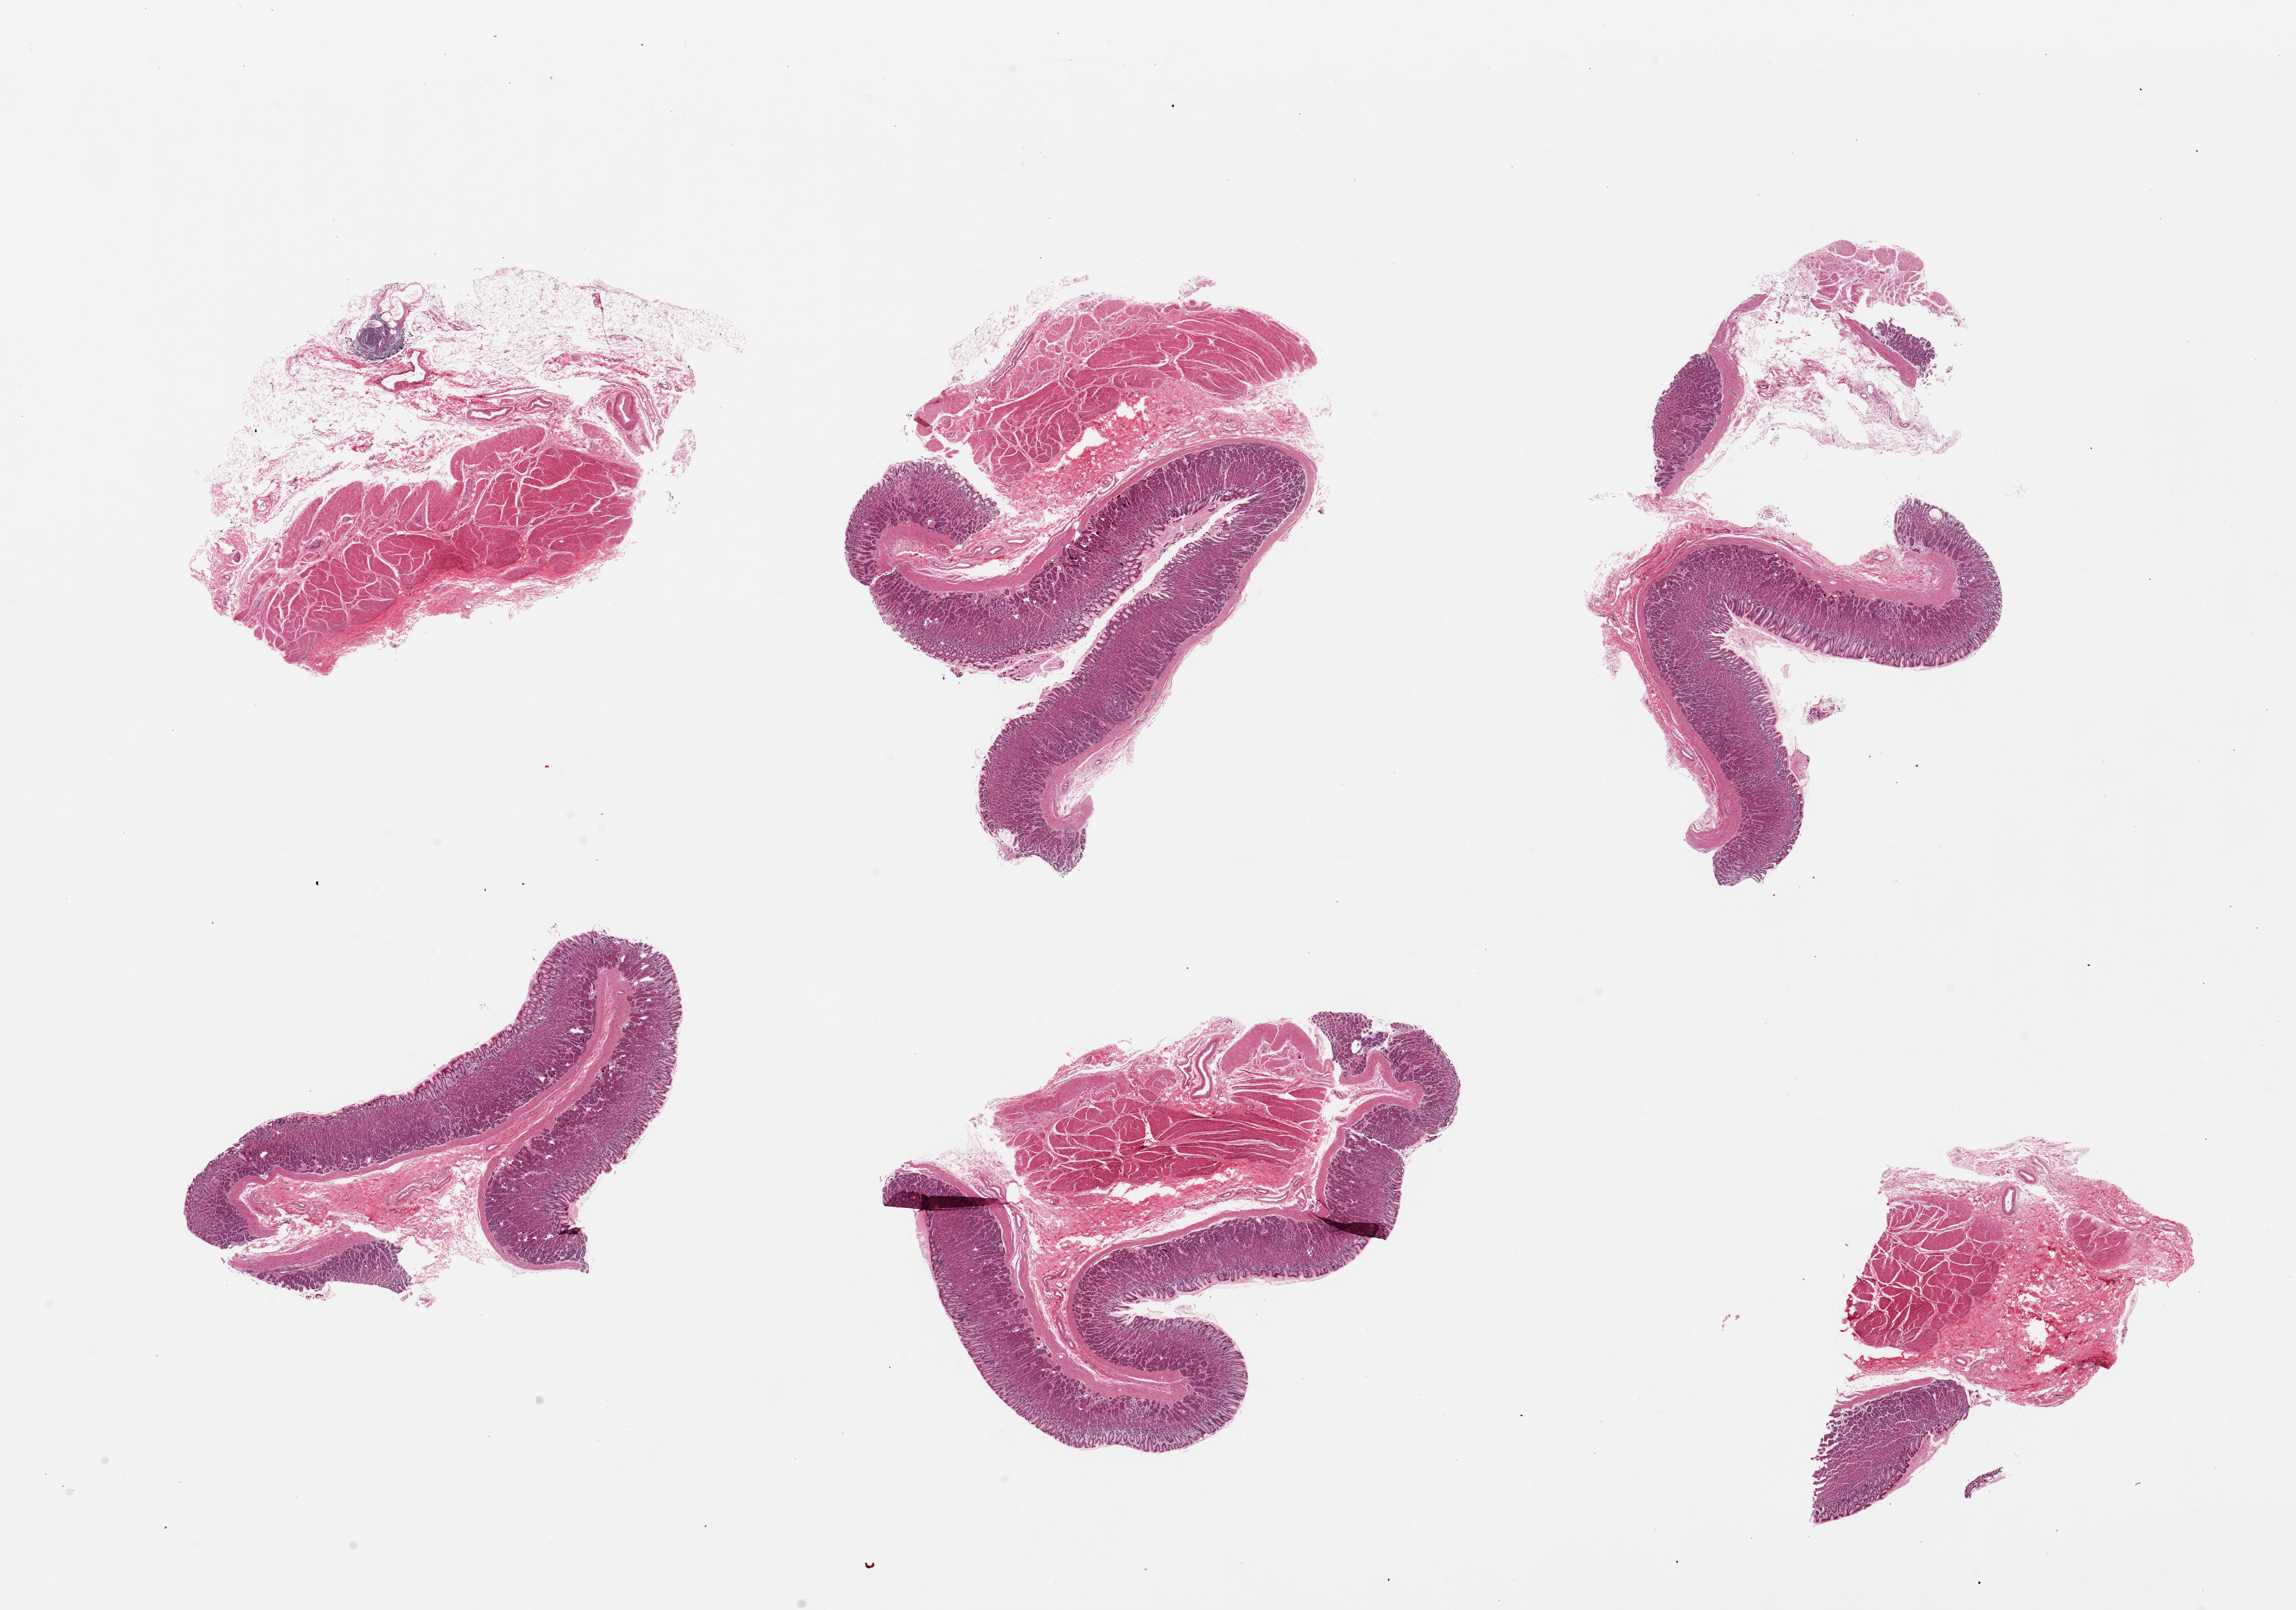
Digitized haematoxylin and eosin-stained section — whole scanned area (about 29.5 x 20.7 mm, from a 20x scan) shown as a low-resolution overview. PAXgene-fixed, paraffin-embedded tissue. Section of stomach (target tissue). Tissue donor sample. Donor: female.
Pathologist's review note for this sample: 1 piece, 7x5mm; mucoa well - preserved, up to 1mm thick.